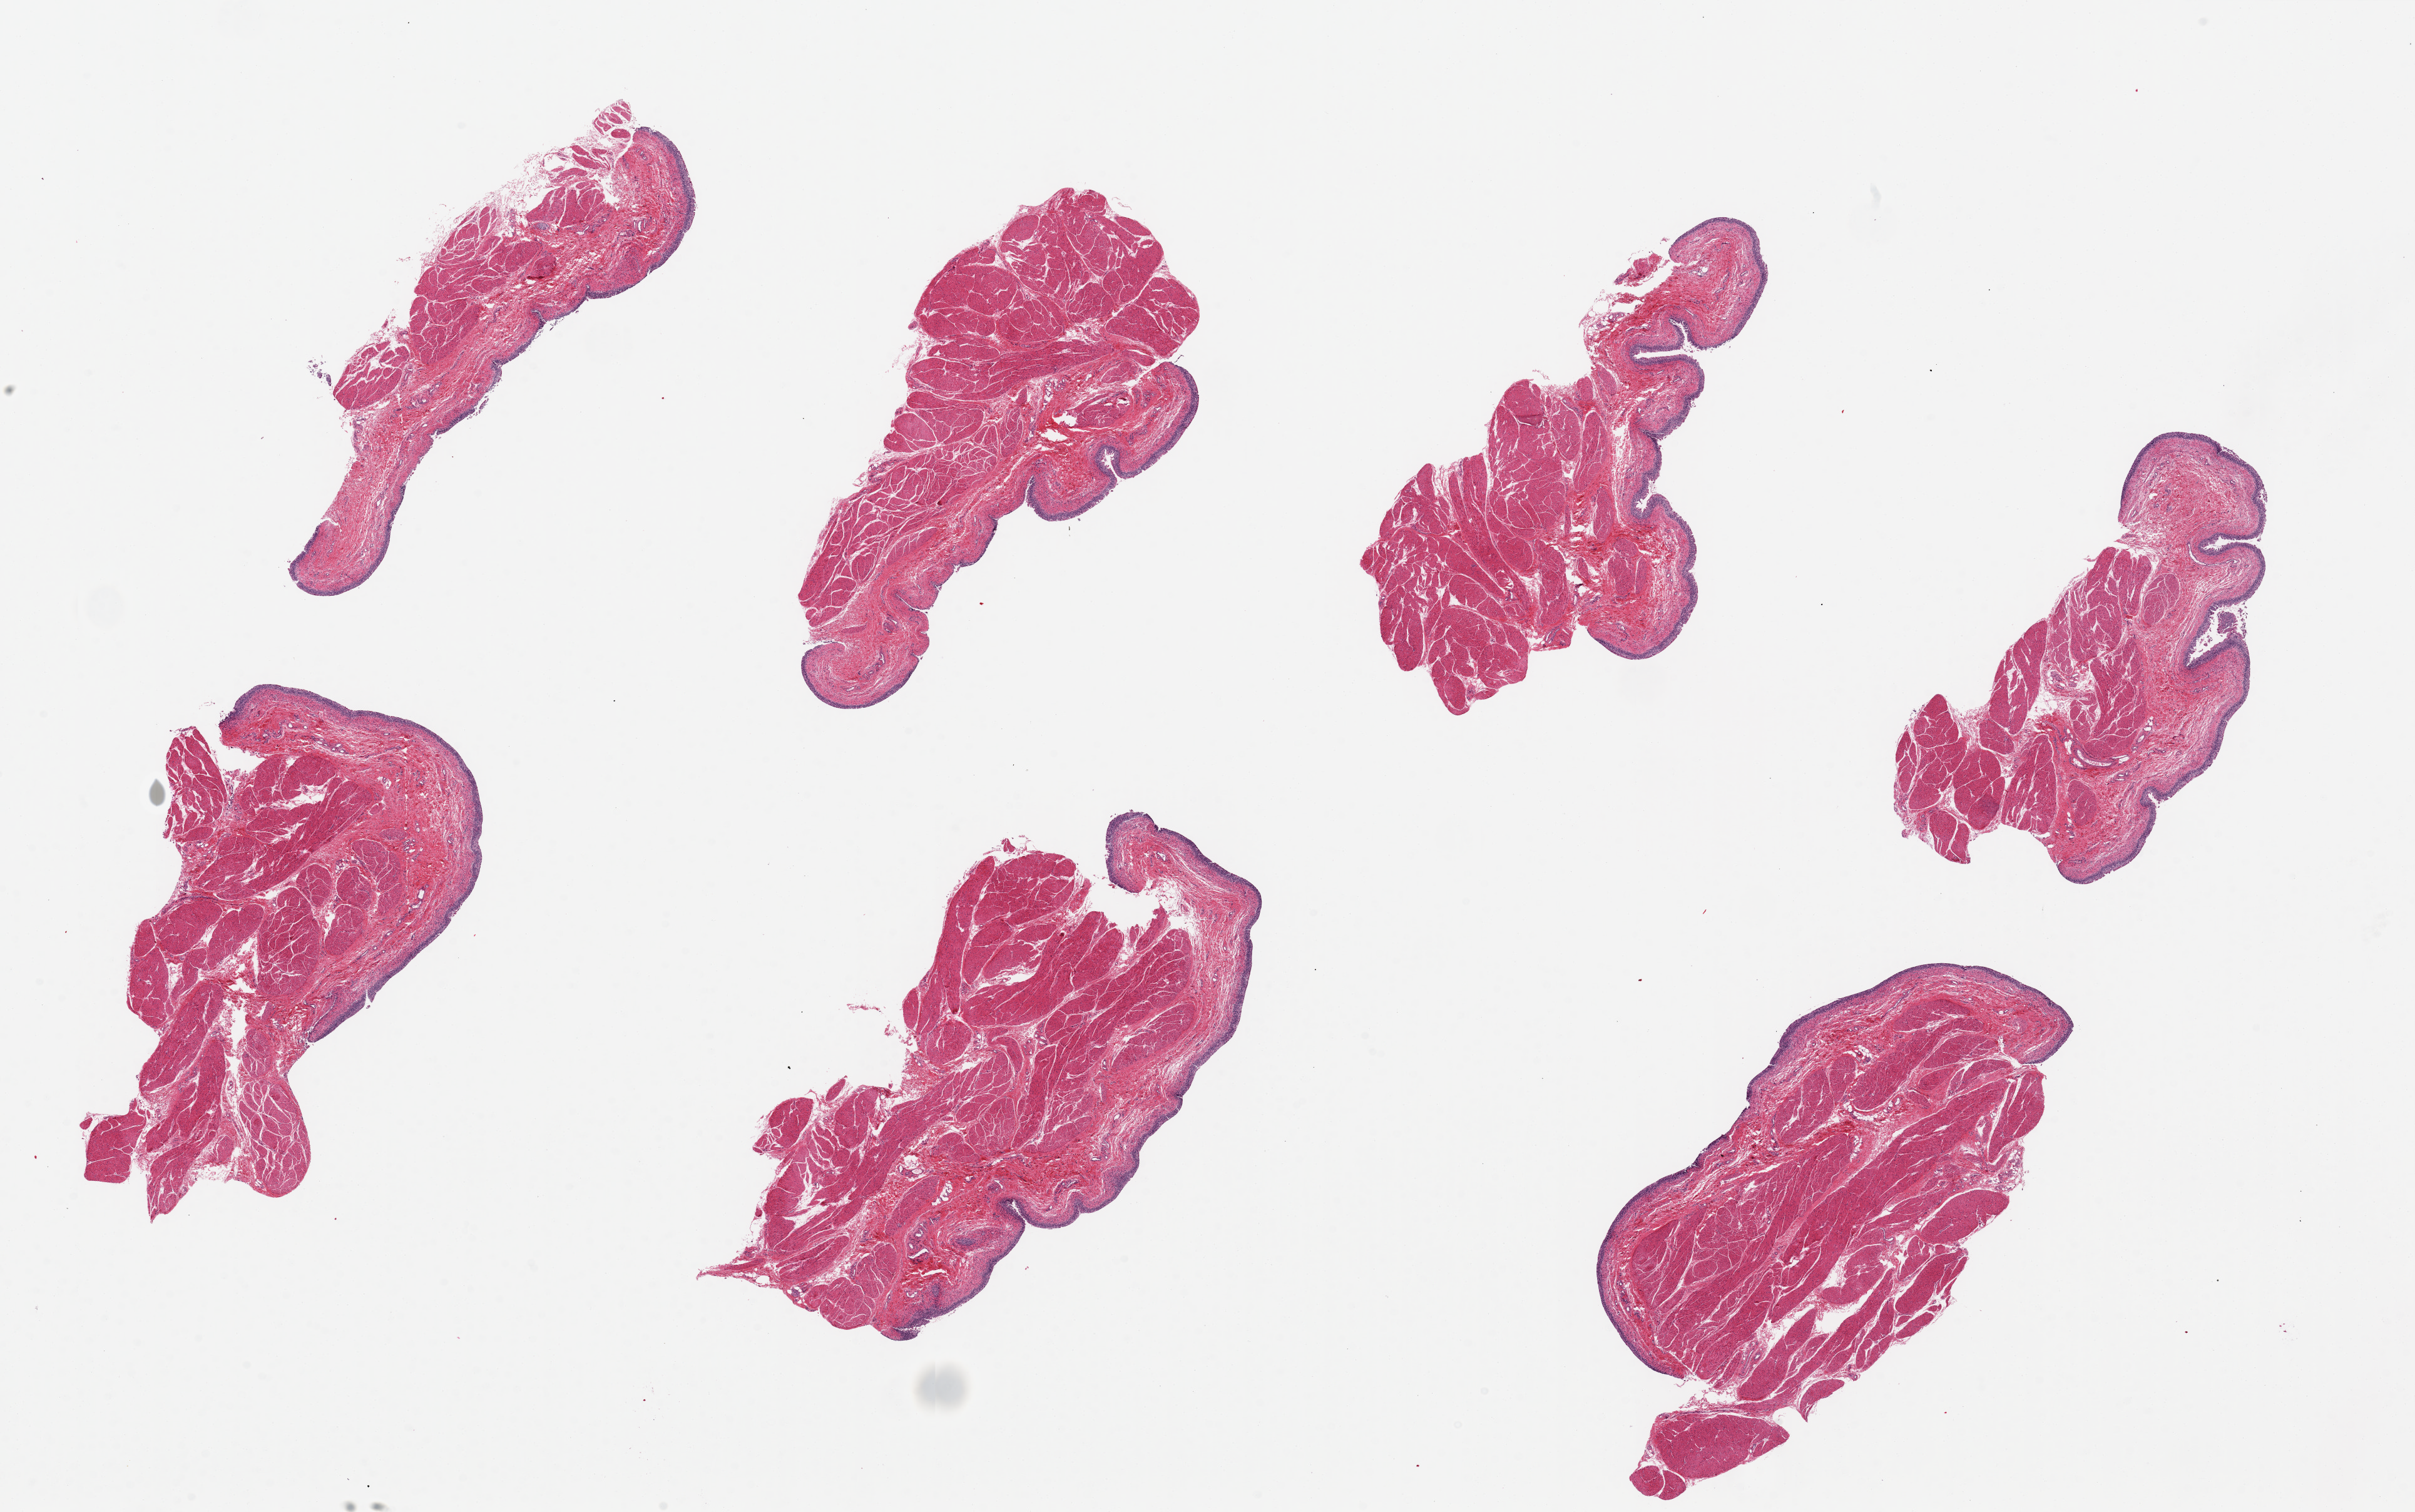
Whole-slide image, H&E stain, brightfield — shown as a low-resolution overview of the whole scanned area (about 30.5 x 19.1 mm, from a 20x scan), PAXgene-fixed paraffin-embedded (PFPE) section, section of urinary bladder (target tissue), donor tissue sample. Donor sex: male.
• reviewer comment on this tissue sample: 7 pieces, ~7x3.5mm. Urothelium remarkably well-preserved, ~2-3% of thickness